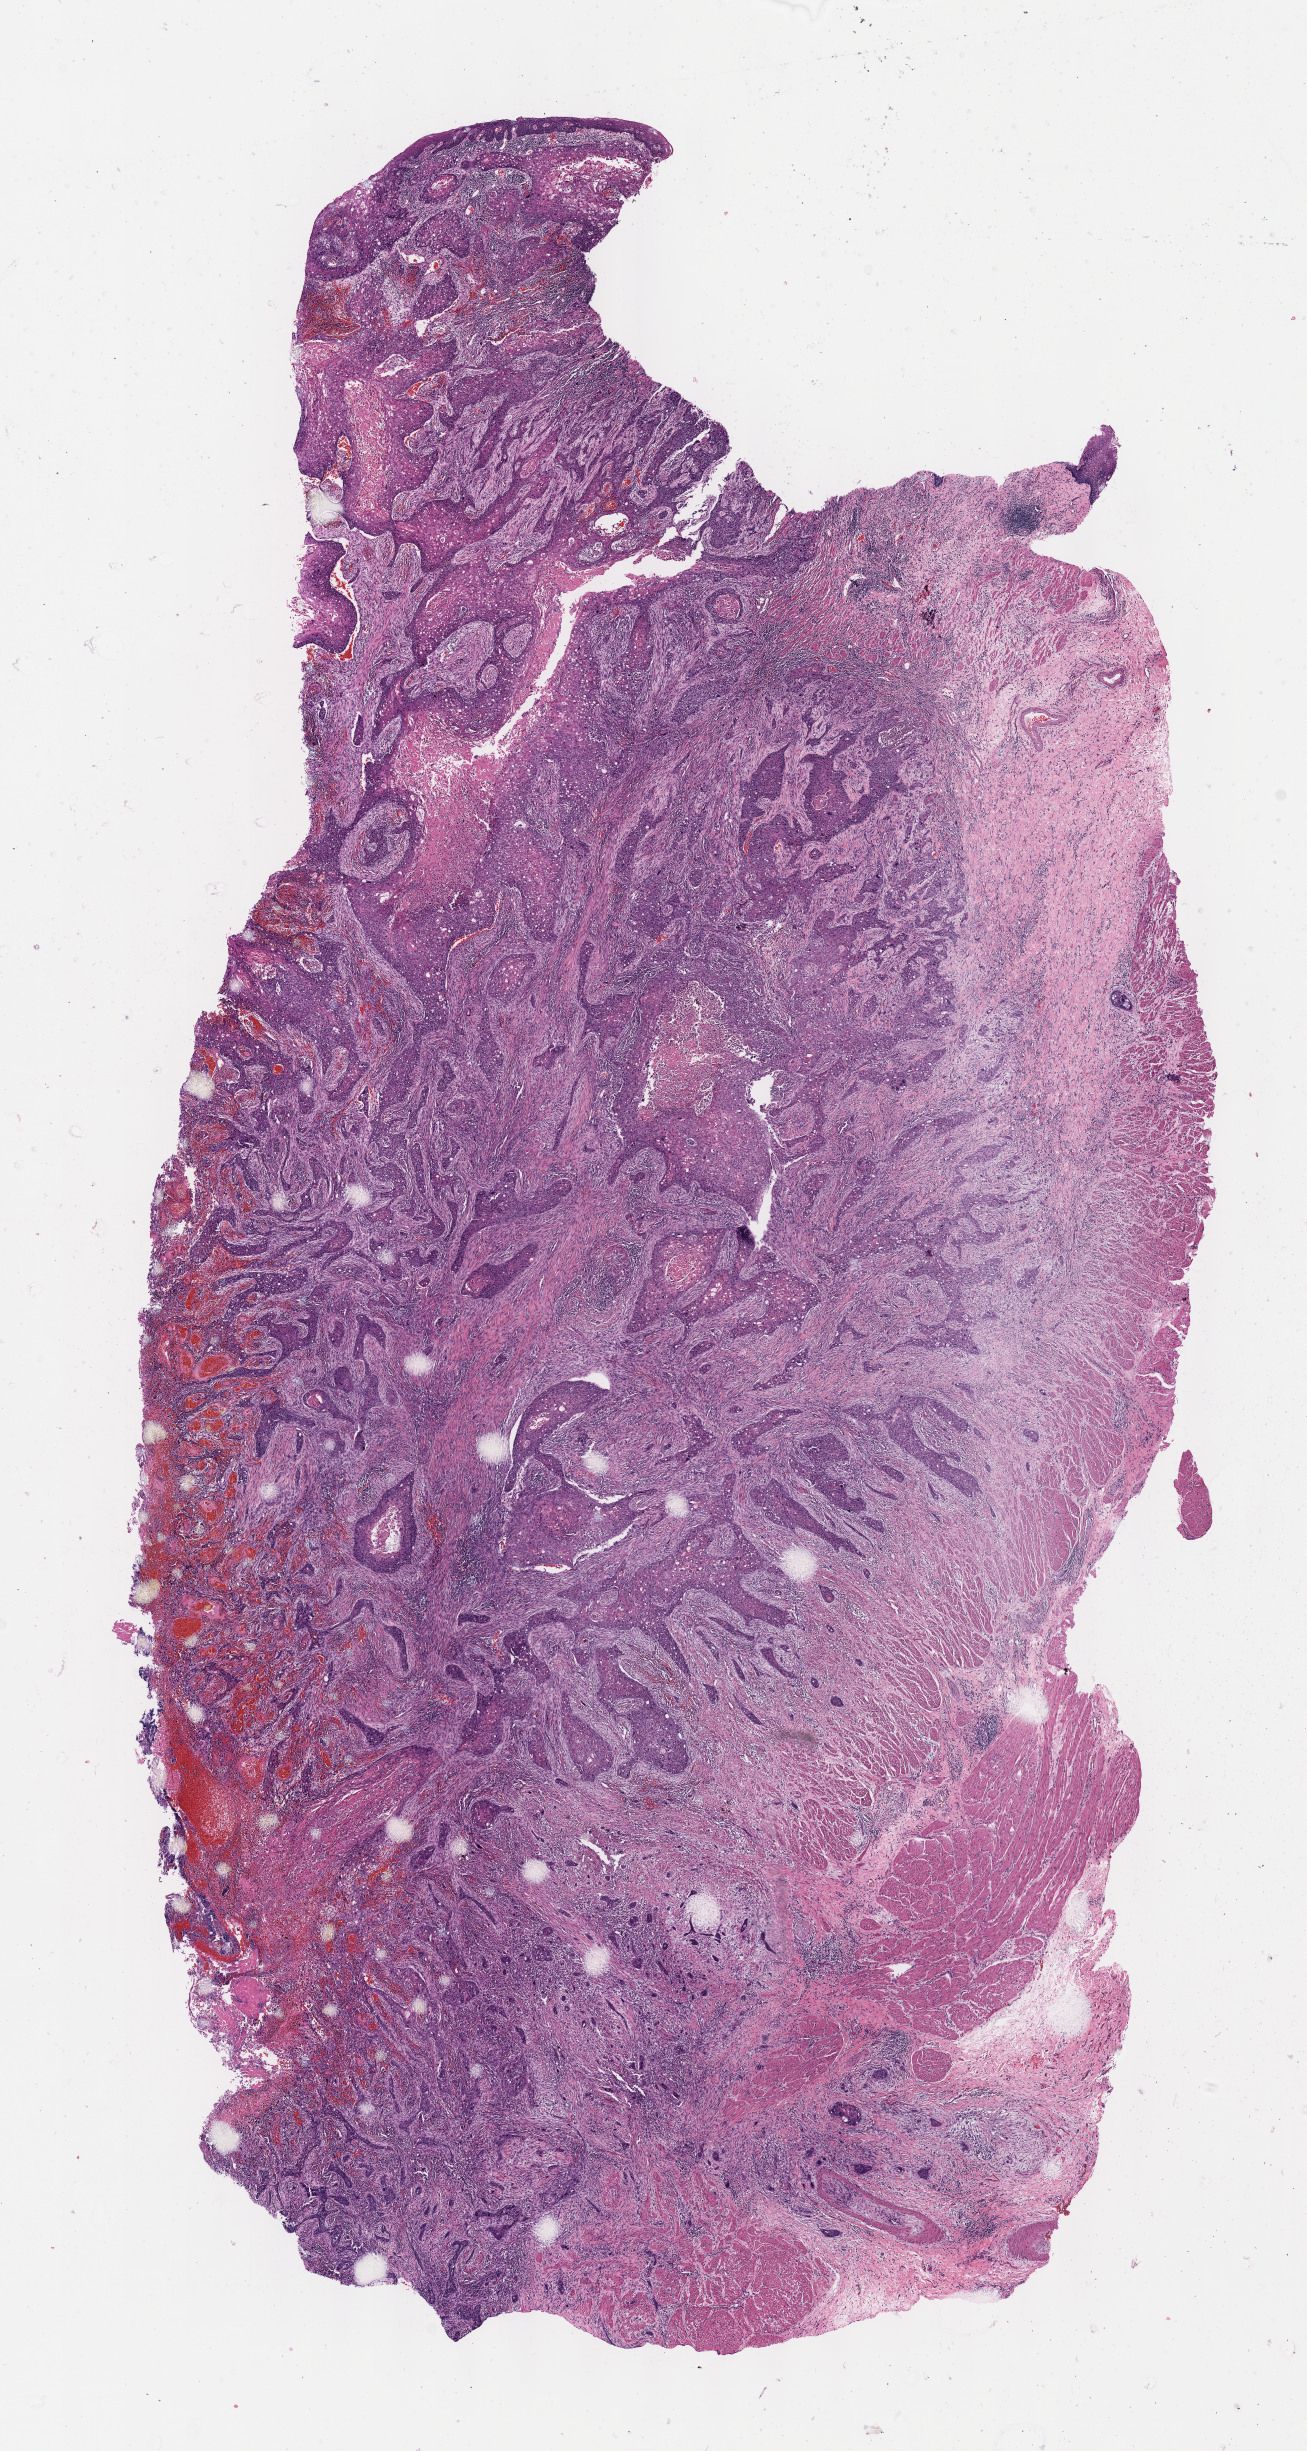
Digitized H&E tissue section (whole slide), whole scanned area (about 10.6 x 19.8 mm) shown as a low-resolution overview, formalin-fixed paraffin-embedded (FFPE) diagnostic section, primary tumour sample from the esophagus. Patient: male, age at initial diagnosis 53 years. Histologic grade: G2 (moderately differentiated).
AJCC pathologic stage: IIB. Pathologic diagnosis: Squamous cell carcinoma, NOS. TNM: T3 N0 M0.